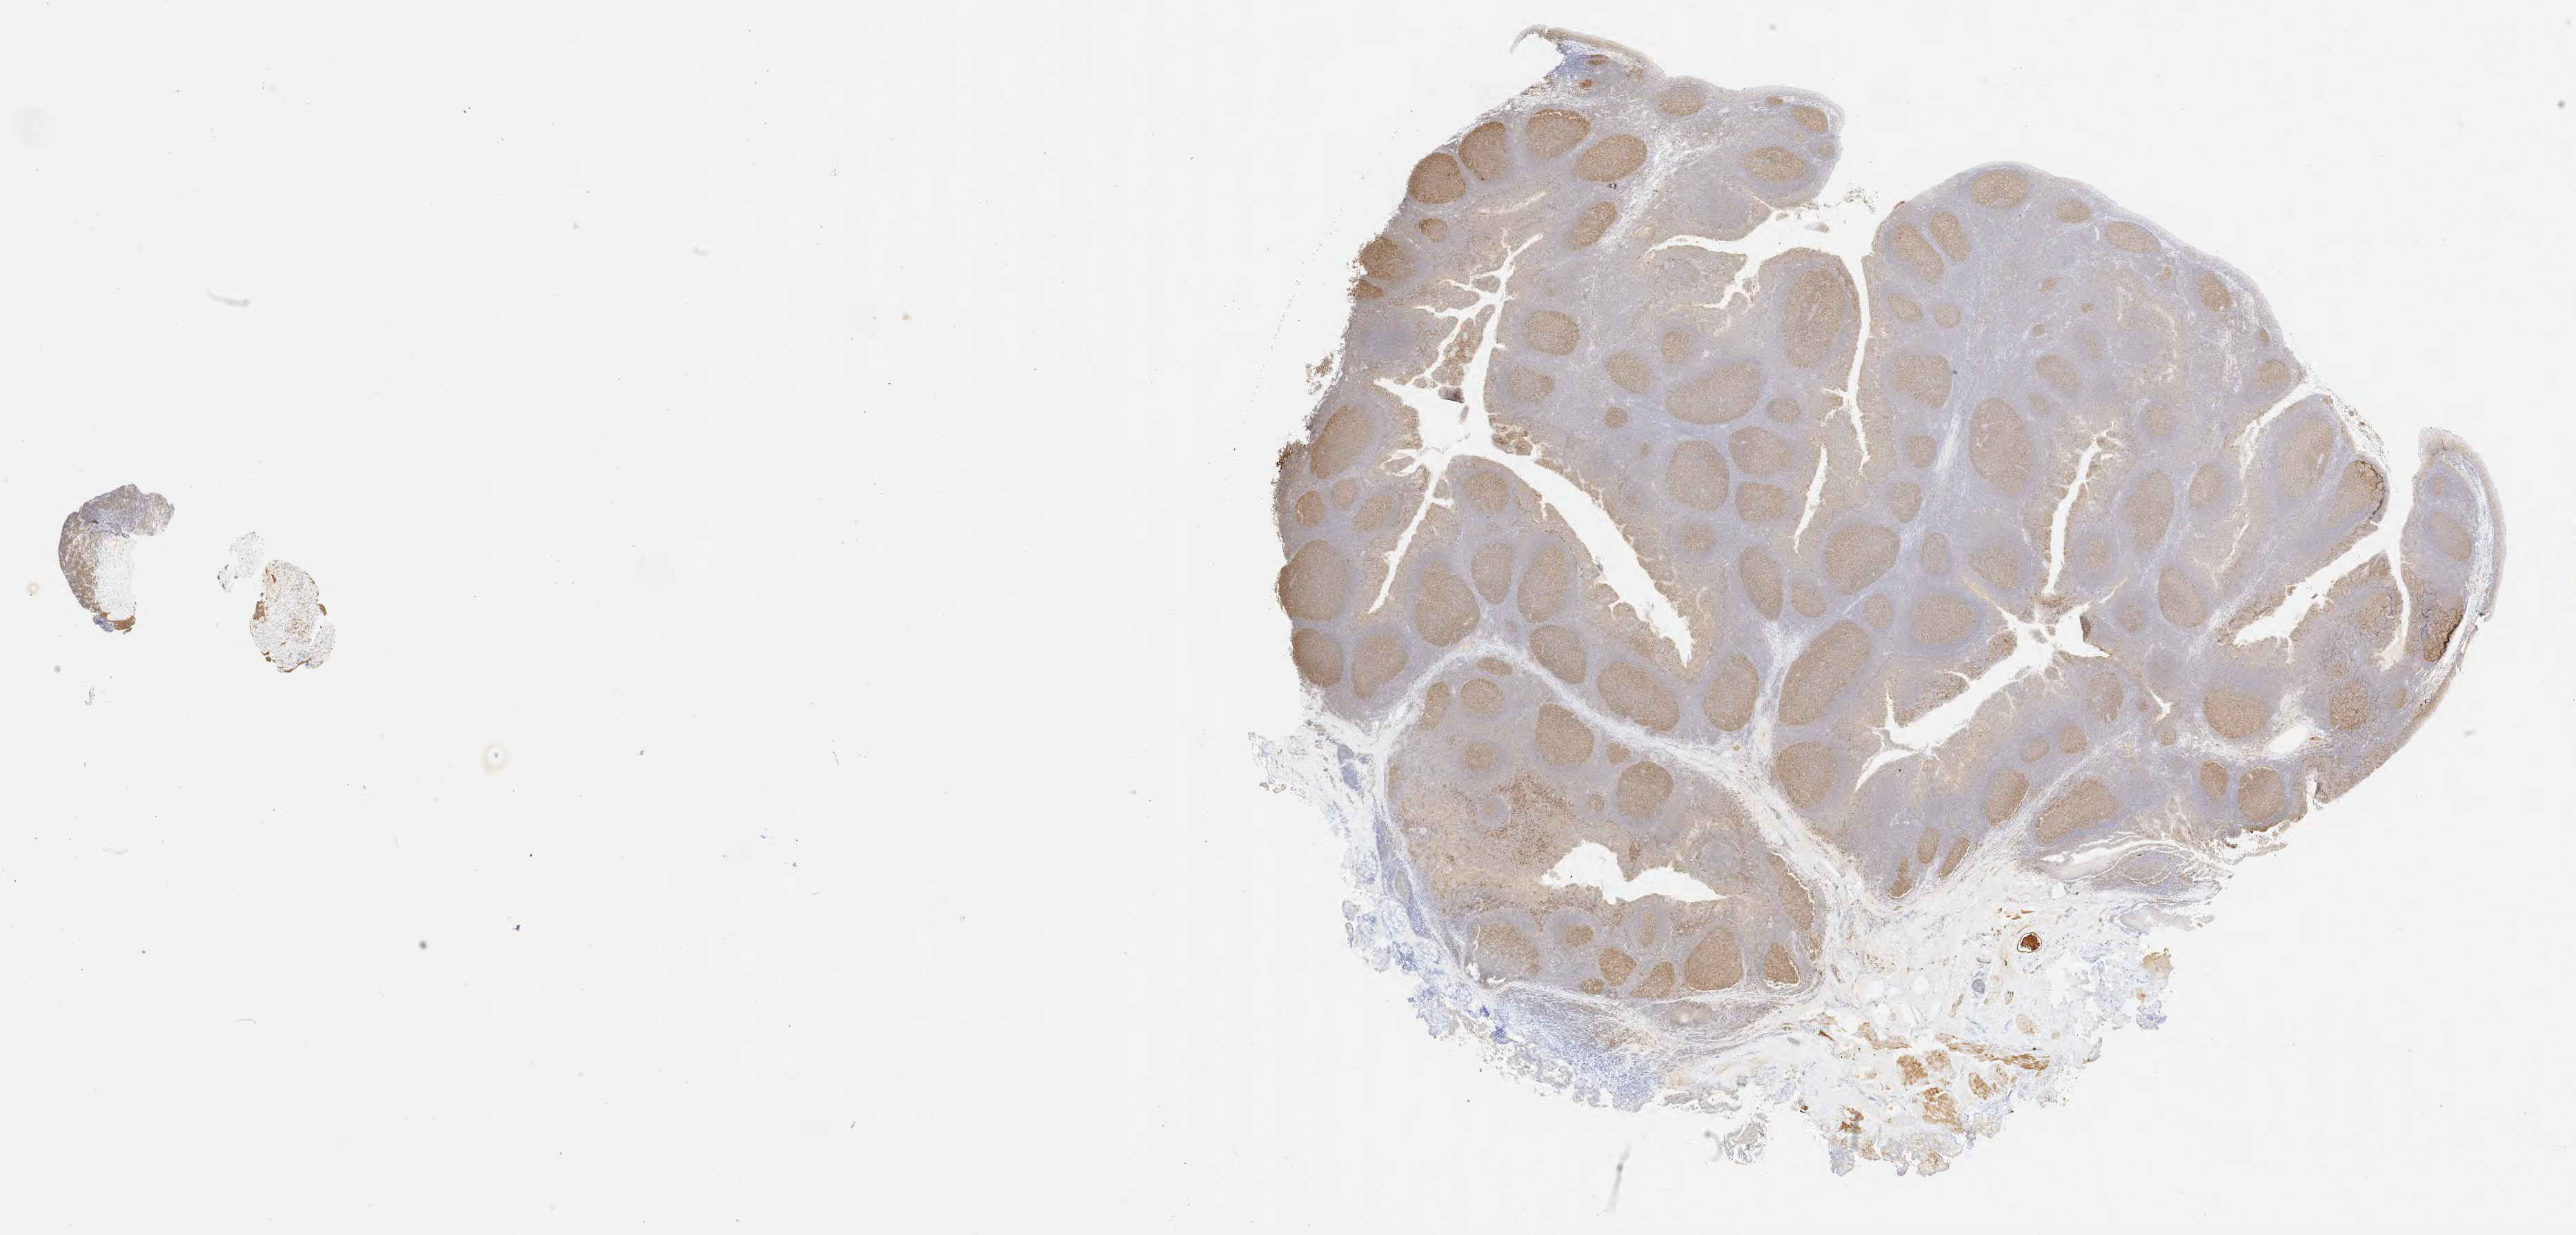
Immunohistochemistry (IHC) whole-slide image stained for BCL6, low-resolution overview of the scanned area, about 30.2 x 14.5 mm, tumor tissue, site: abdomen proper. Patient: female, age at initial diagnosis 6 years.
Diagnosis: Diffuse large B-cell lymphoma, NOS.